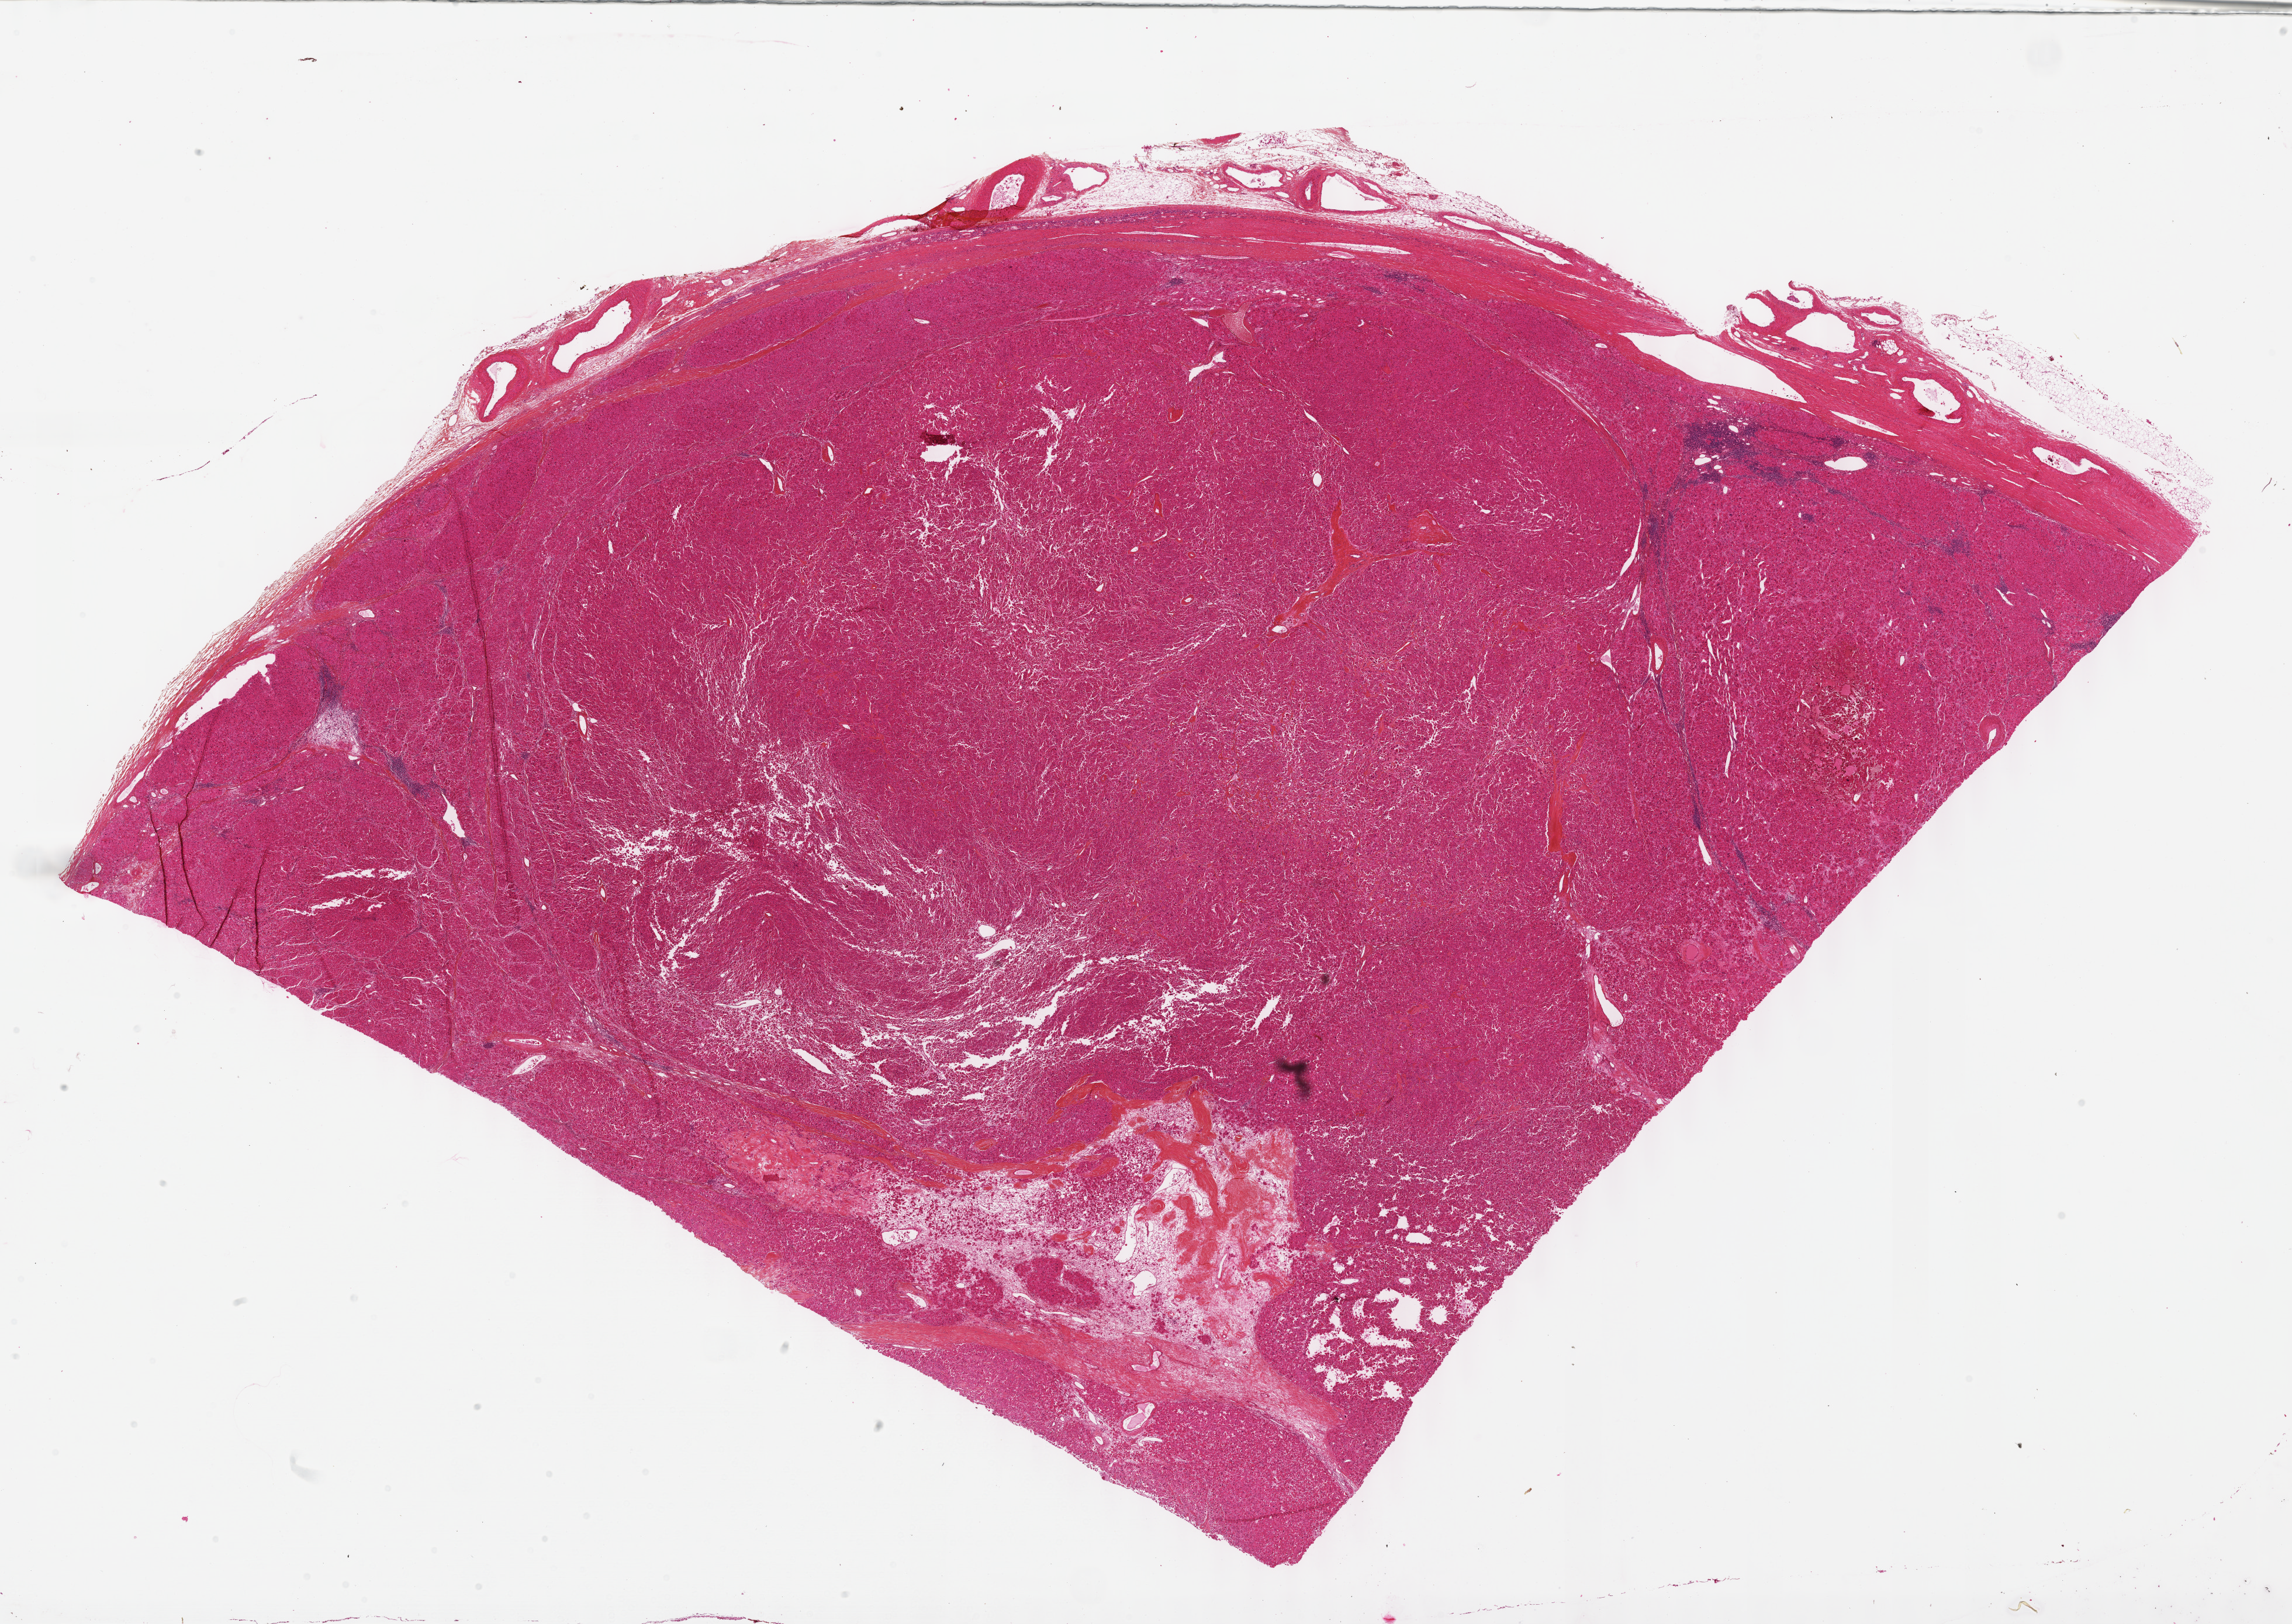
Digitized H&E-stained tissue section (whole slide) — low-resolution overview of the scanned area, about 31.7 x 22.5 mm (from a 40x scan); formalin-fixed paraffin-embedded (FFPE) diagnostic section; adrenal cortex, primary tumour sample. Female, age 37 years at initial diagnosis.
Lymph nodes positive (case pathology): 0 of 21 examined. Laterality: right. Diagnosis: Adrenal cortical carcinoma (cortex of adrenal gland).